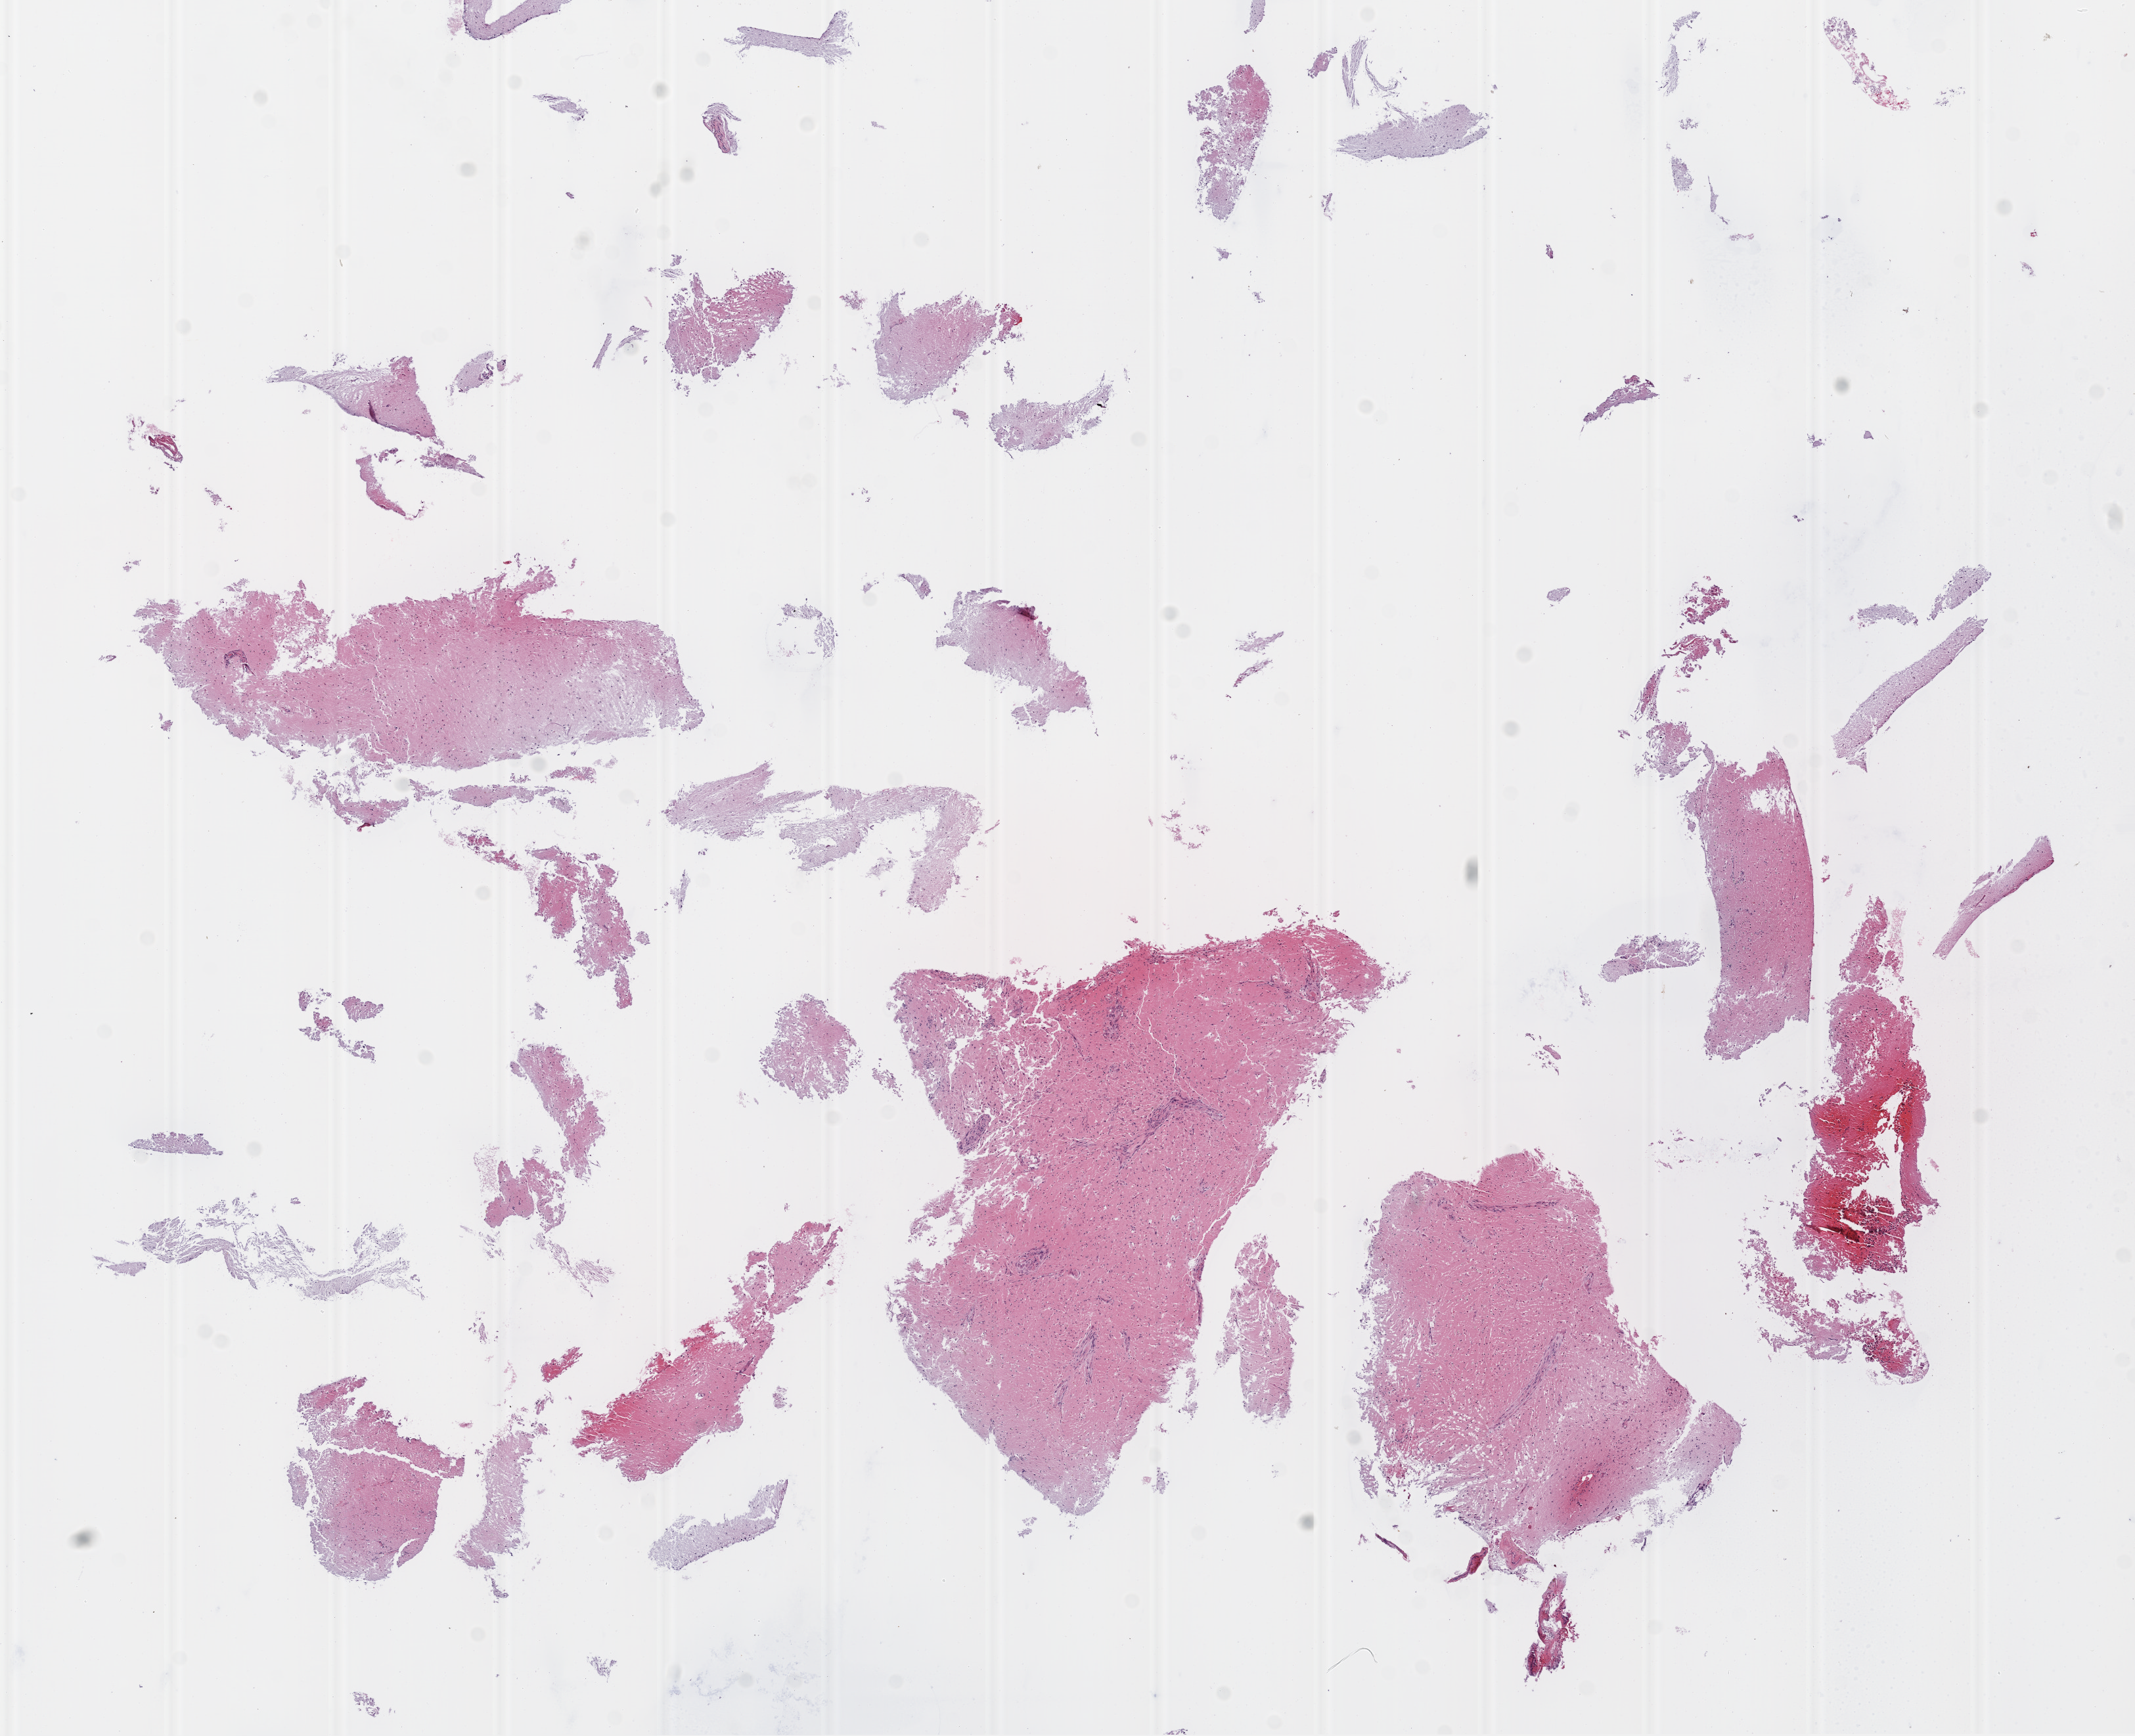
Whole-slide histology image, Hematoxylin and eosin (H&E) stained — a low-resolution overview of the entire scanned area, about 13.0 x 10.6 mm (slide scanned at 20x); FFPE section; sample: primary tumour, brain. Male, age 75 years at initial diagnosis.
Diagnosis: Glioblastoma.